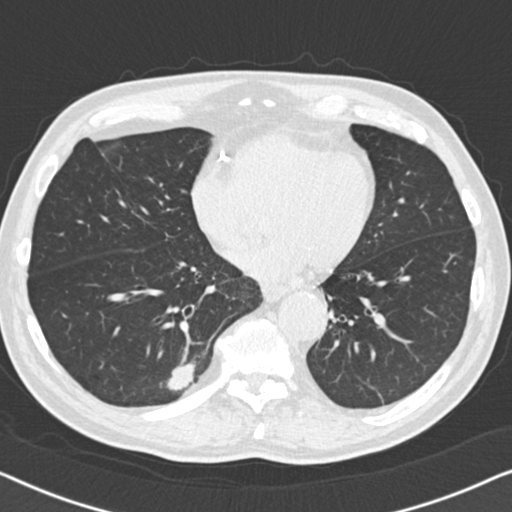
Low-dose screening chest CT, one axial slice. Position 53 of 164 along the scan axis. Reconstruction kernel B30f. 120 kVp. Lung window (W 1500 / L -600 HU). 512 × 512 image matrix, field of view 330 × 330 mm.
Annotated regions visible in this slice (manually delineated by an expert):
- lesion 1 (tumor, lower lobe of right lung): bounding box [x1, y1, x2, y2] px = [167, 361, 196, 391]